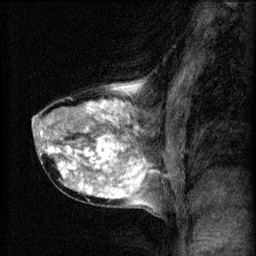
Breast MRI (dynamic contrast-enhanced), one sagittal slice. Slice 35 of 60 in the series (ordered by position). 3 images stored at this slice position (order not interpretable as contrast timing). 1.5 T. TE 4.2 ms, TR 8.2 ms. 2 mm slice thickness. 256 × 256 image matrix, field of view 180 × 180 mm. Patient: female, 40 years.
Annotated regions visible in this slice (semi-automatic segmentation, software-assisted and operator-edited):
- analysis volume of interest (the breast-tissue region the enhancement analysis was run in; not a lesion): bounding box [x1, y1, x2, y2] px = [32, 80, 167, 211]
- tumour enhancement mask (voxels above the 70 % enhancement threshold inside the analysis volume of interest): [33, 86, 155, 199]